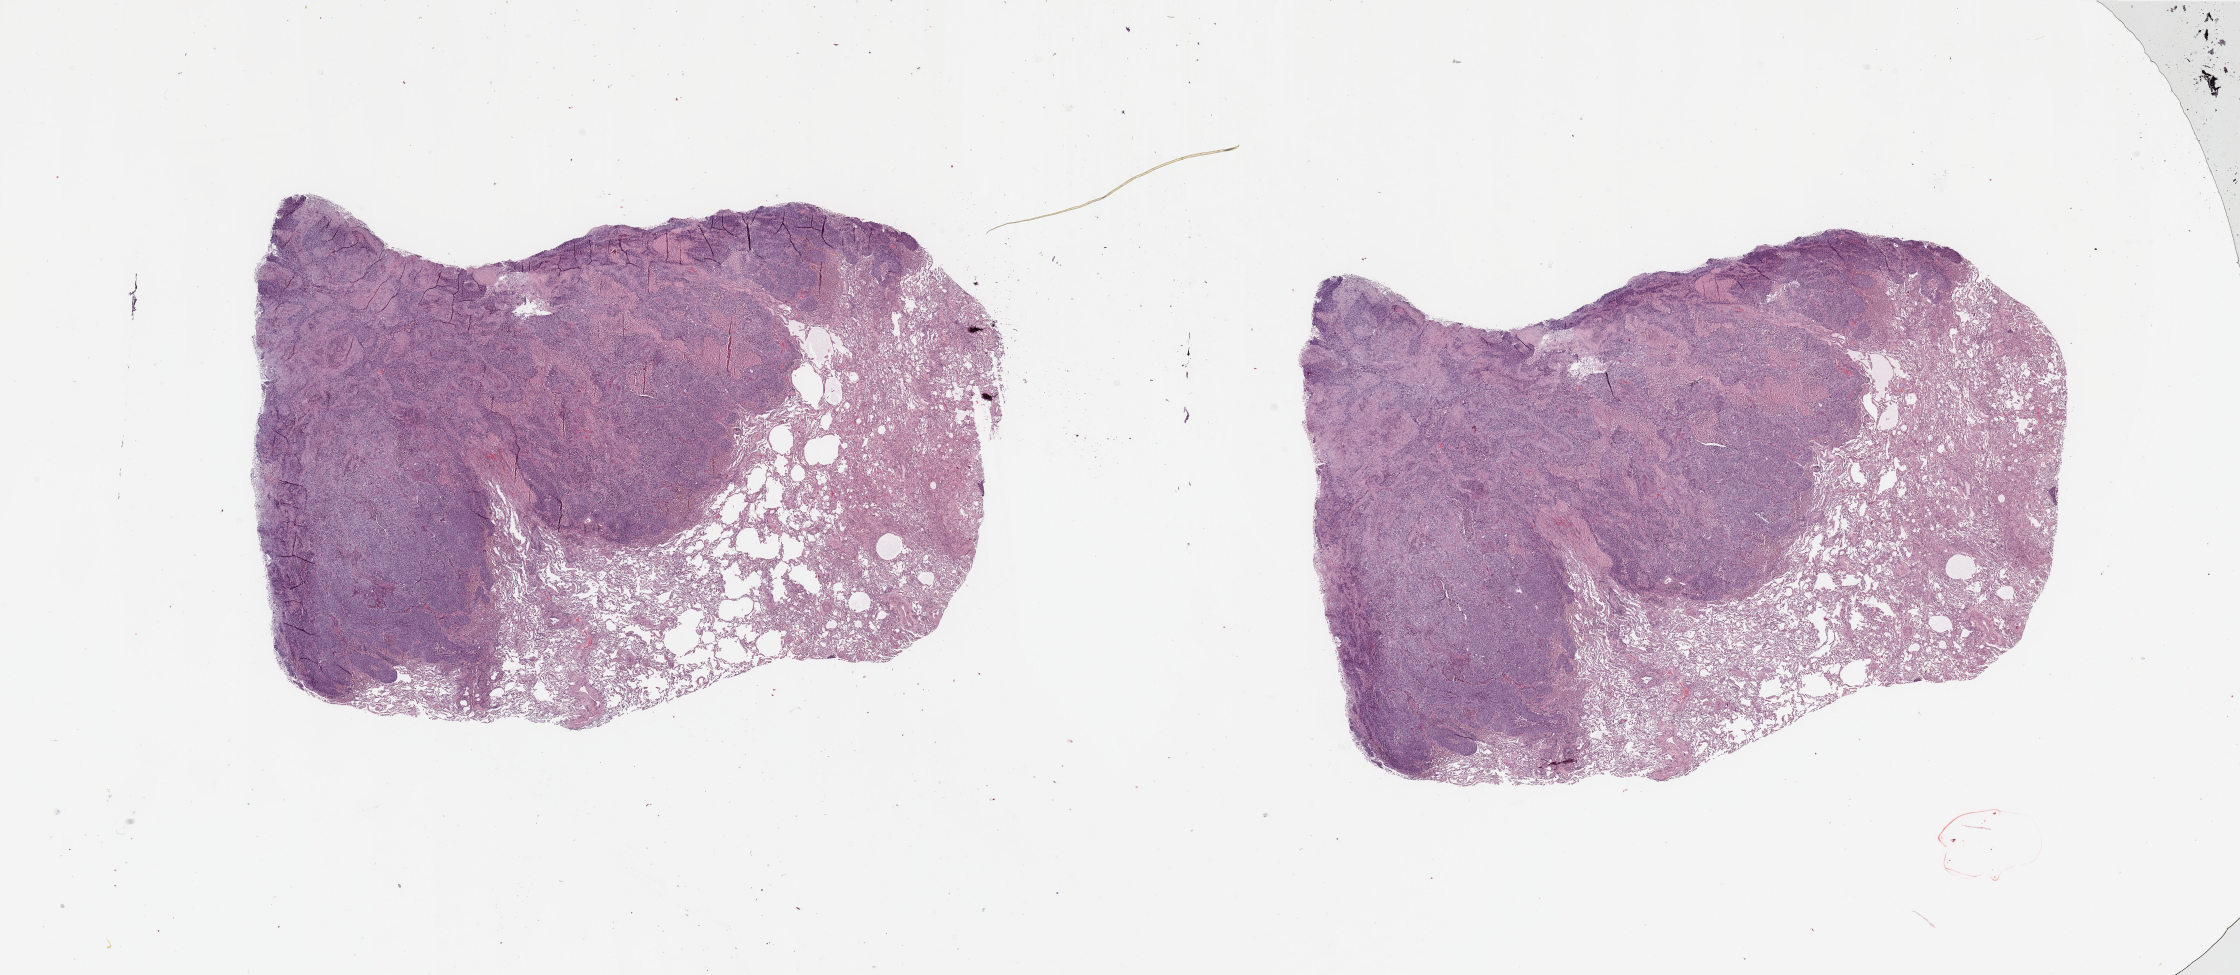
Digitized Hematoxylin and eosin (H&E) stained tissue section (whole slide) — low-resolution overview of the scanned area, about 35.4 x 15.4 mm (slide scanned at 20x); tumour tissue sample, sampled site: lung. 57-year-old male patient. Histologic grade: G3 (poorly differentiated). Slide review estimates, as recorded: tumour nuclei 70%, necrosis 15%.
AJCC pathologic stage: IA. Primary tumour site (as recorded): right lower lobe. Histologic diagnosis: Squamous cell carcinoma, NOS.